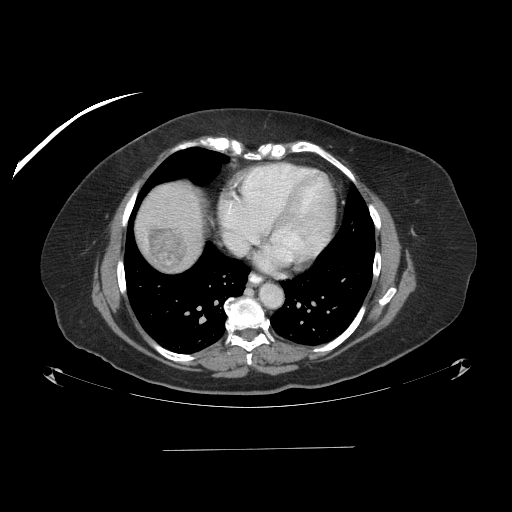
Contrast-enhanced abdominal CT (liver protocol), one axial slice. Position 84 of 103 along the scan axis. Reconstruction kernel STANDARD. One of 2 acquisitions stored at this slice position. Soft-tissue window (W 400 / L 40 HU). 2.5 mm slice thickness. 512 × 512 image matrix. Case-level facts recorded for this patient, not image findings: diagnosis: hepatocellular carcinoma (patient treated with transarterial chemoembolisation; whether this scan precedes or follows treatment is not stated here); TNM stage (as recorded): Stage-IIIA; Child-Pugh class: A; tumour differentiation: poorly differentiated; tumour nodularity: multinodular.
Outlined on this slice (semi-automatically segmented with operator editing):
- liver parenchyma outside the tumour (the mass and vessels are separate outlines, so this box may not span the whole liver): bounding box (x1, y1, x2, y2) in pixels: (136, 182, 202, 271)
- mass: (147, 227, 187, 269)